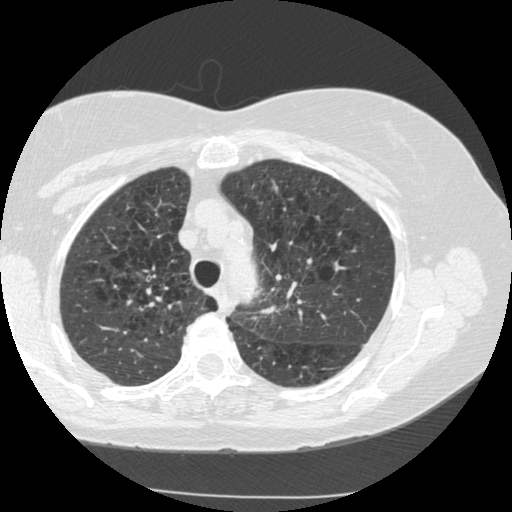
Low-dose screening chest CT, axial slice, second annual screen, lung window (W 1500 / L -600 HU), standard (soft-tissue) reconstruction kernel (STANDARD), 120 kVp, 512 × 512 image matrix. Female participant, aged 70 years at enrolment. Current smoker at enrolment.
Expert-annotated lung lesion, bounding box [x1, y1, x2, y2] px = [233, 271, 293, 337]. The exam's reader record, not a measurement of the box and not confirmed to be the same lesion: non-calcified nodule or mass ≥4 mm, left upper lobe, 15 × 13 mm, spiculated (stellate) margins, soft tissue attenuation, pre-existing on the prior screen: yes; interval growth: yes. Official screen result: positive, other. Participant outcome: lung cancer diagnosed 360 days after this screen — neoplasm, malignant, left upper lobe, stage IIIB (AJCC 6th edition), 40 mm at pathology.